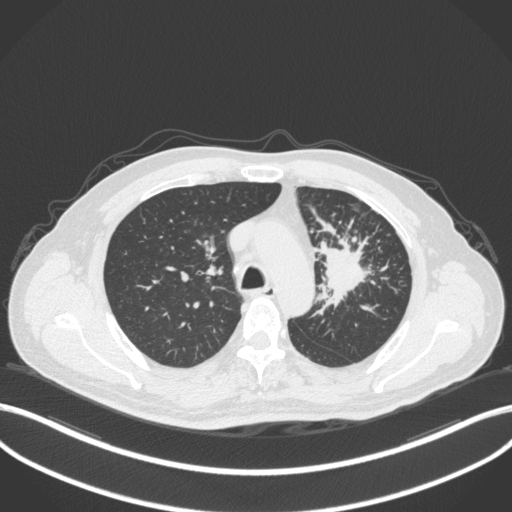
Chest CT, one axial slice. Position 256 of 386 along the scan axis. 120 kVp. Lung window (W 1500 / L -600 HU). 512 × 512 image matrix, field of view 400 × 400 mm. Patient: male, 69 years. From the clinical record (not read from this slice): clinical TNM (as recorded): T2a N2 M0.
Structures marked on this image (rectangle marked by the reading radiologist):
- lung tumour (recorded histology: adenocarcinoma): bounding box [x1, y1, x2, y2] px = [314, 229, 376, 313]